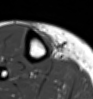
MRI of an extremity soft-tissue mass, one axial slice. Position 13 of 54 along the scan axis. MR volume resampled by the dataset authors to the PET/CT grid (not the native acquisition matrix). 93 × 99 image matrix, field of view 91 × 97 mm. Female patient. Case-level facts recorded for this patient, not image findings: histological type: undifferentiated – high grade; grade: high; site of the primary tumour: right thigh.
Annotated regions visible in this slice (expert contour drawn on MRI and transferred to this co-registered scan by the dataset authors):
- gross tumour volume (mass): box from (x=38, y=30) to (x=55, y=51) px